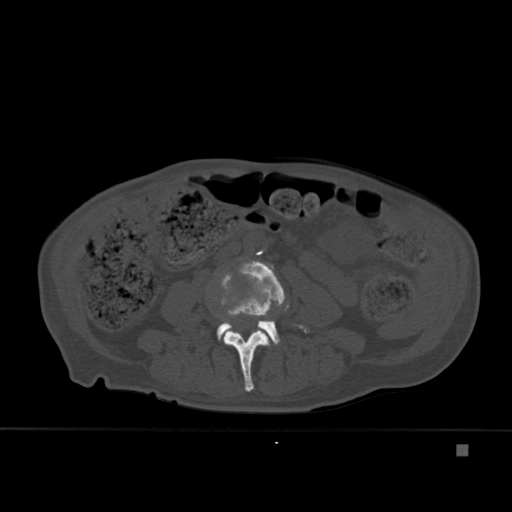
CT including the spine, one axial slice; position 135 of 451 along the scan axis; bone window (W 1800 / L 400 HU); 1.5 mm slice thickness; 512 × 512 image matrix, field of view 378 × 378 mm. Patient: male, 75 years. From the clinical record (not read from this slice): primary cancer: prostate.
Annotated regions visible in this slice (semi-automatically segmented with operator editing):
- L3 vertebra: bounding box (x1, y1, x2, y2) in pixels: (218, 274, 271, 392)
- L4 vertebra: (217, 260, 307, 345)